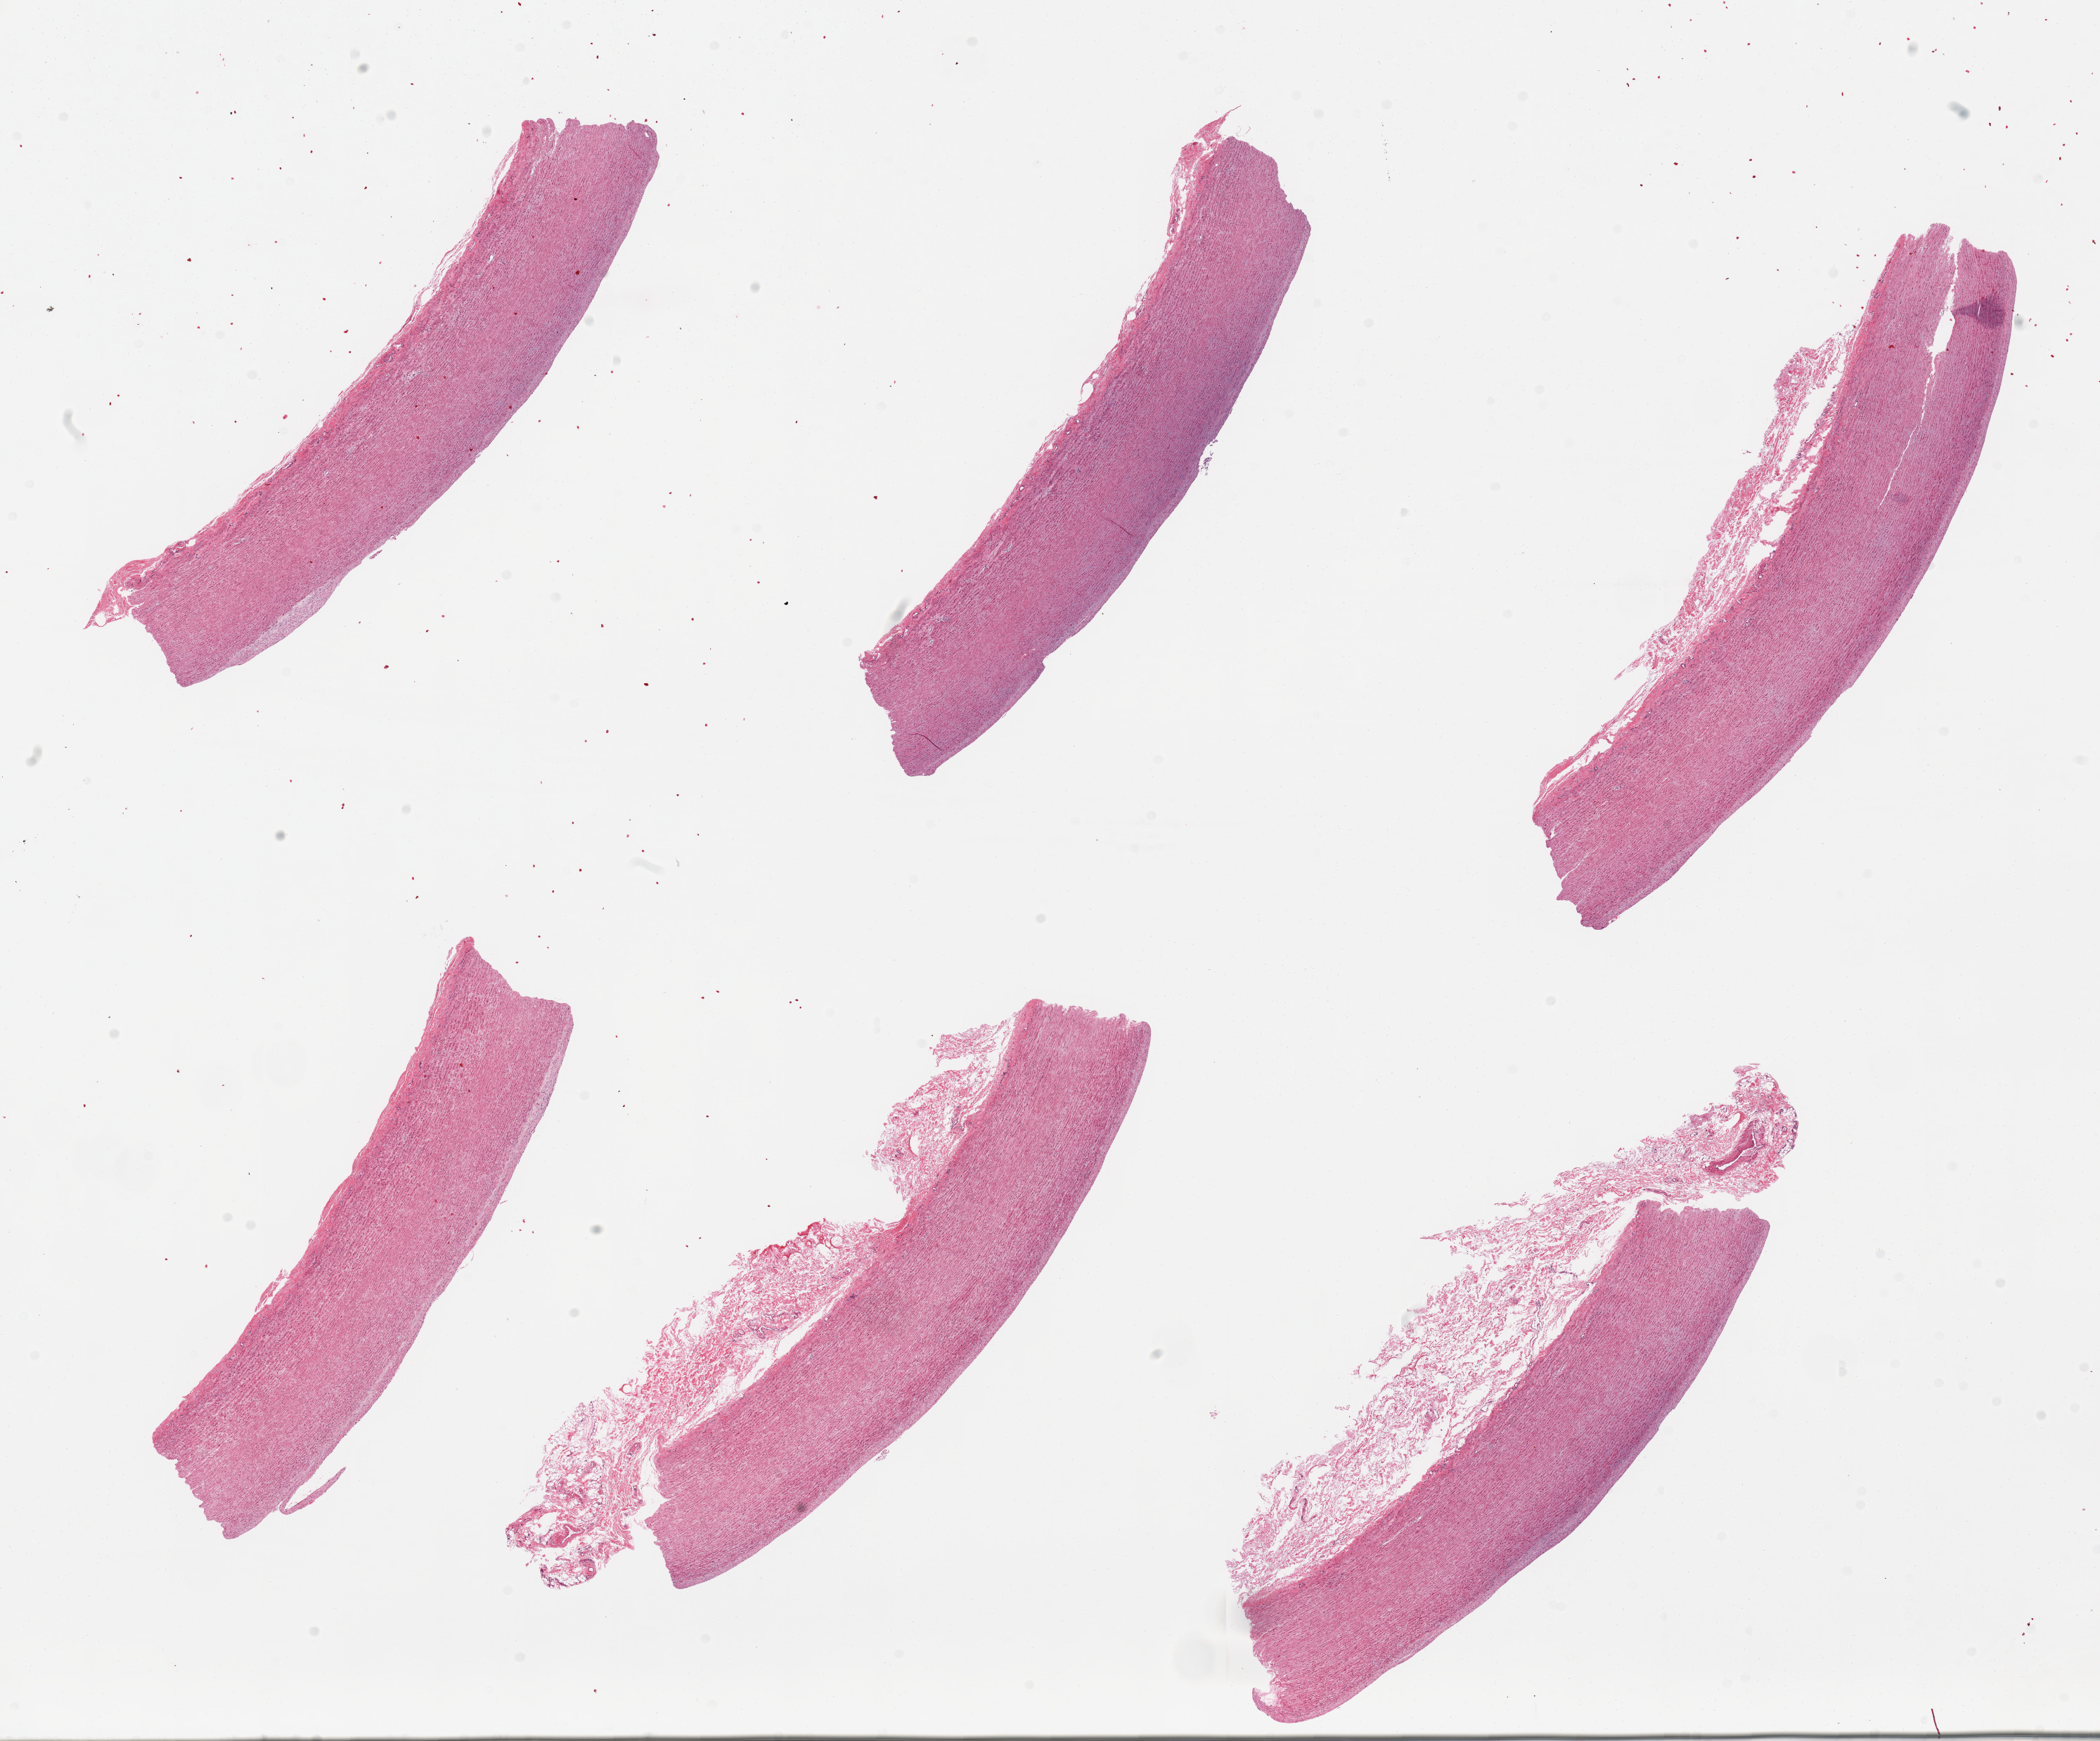
H&E whole-slide image, shown as a low-resolution overview of the whole scanned area (about 23.6 x 19.6 mm, from a 20x scan). PAXgene-fixed paraffin-embedded (PFPE) section. Sampled site (target tissue): aorta. Donor tissue sample. Donor: male.
Pathologist's review note for this sample: 6 pieces, some intimal thickening.